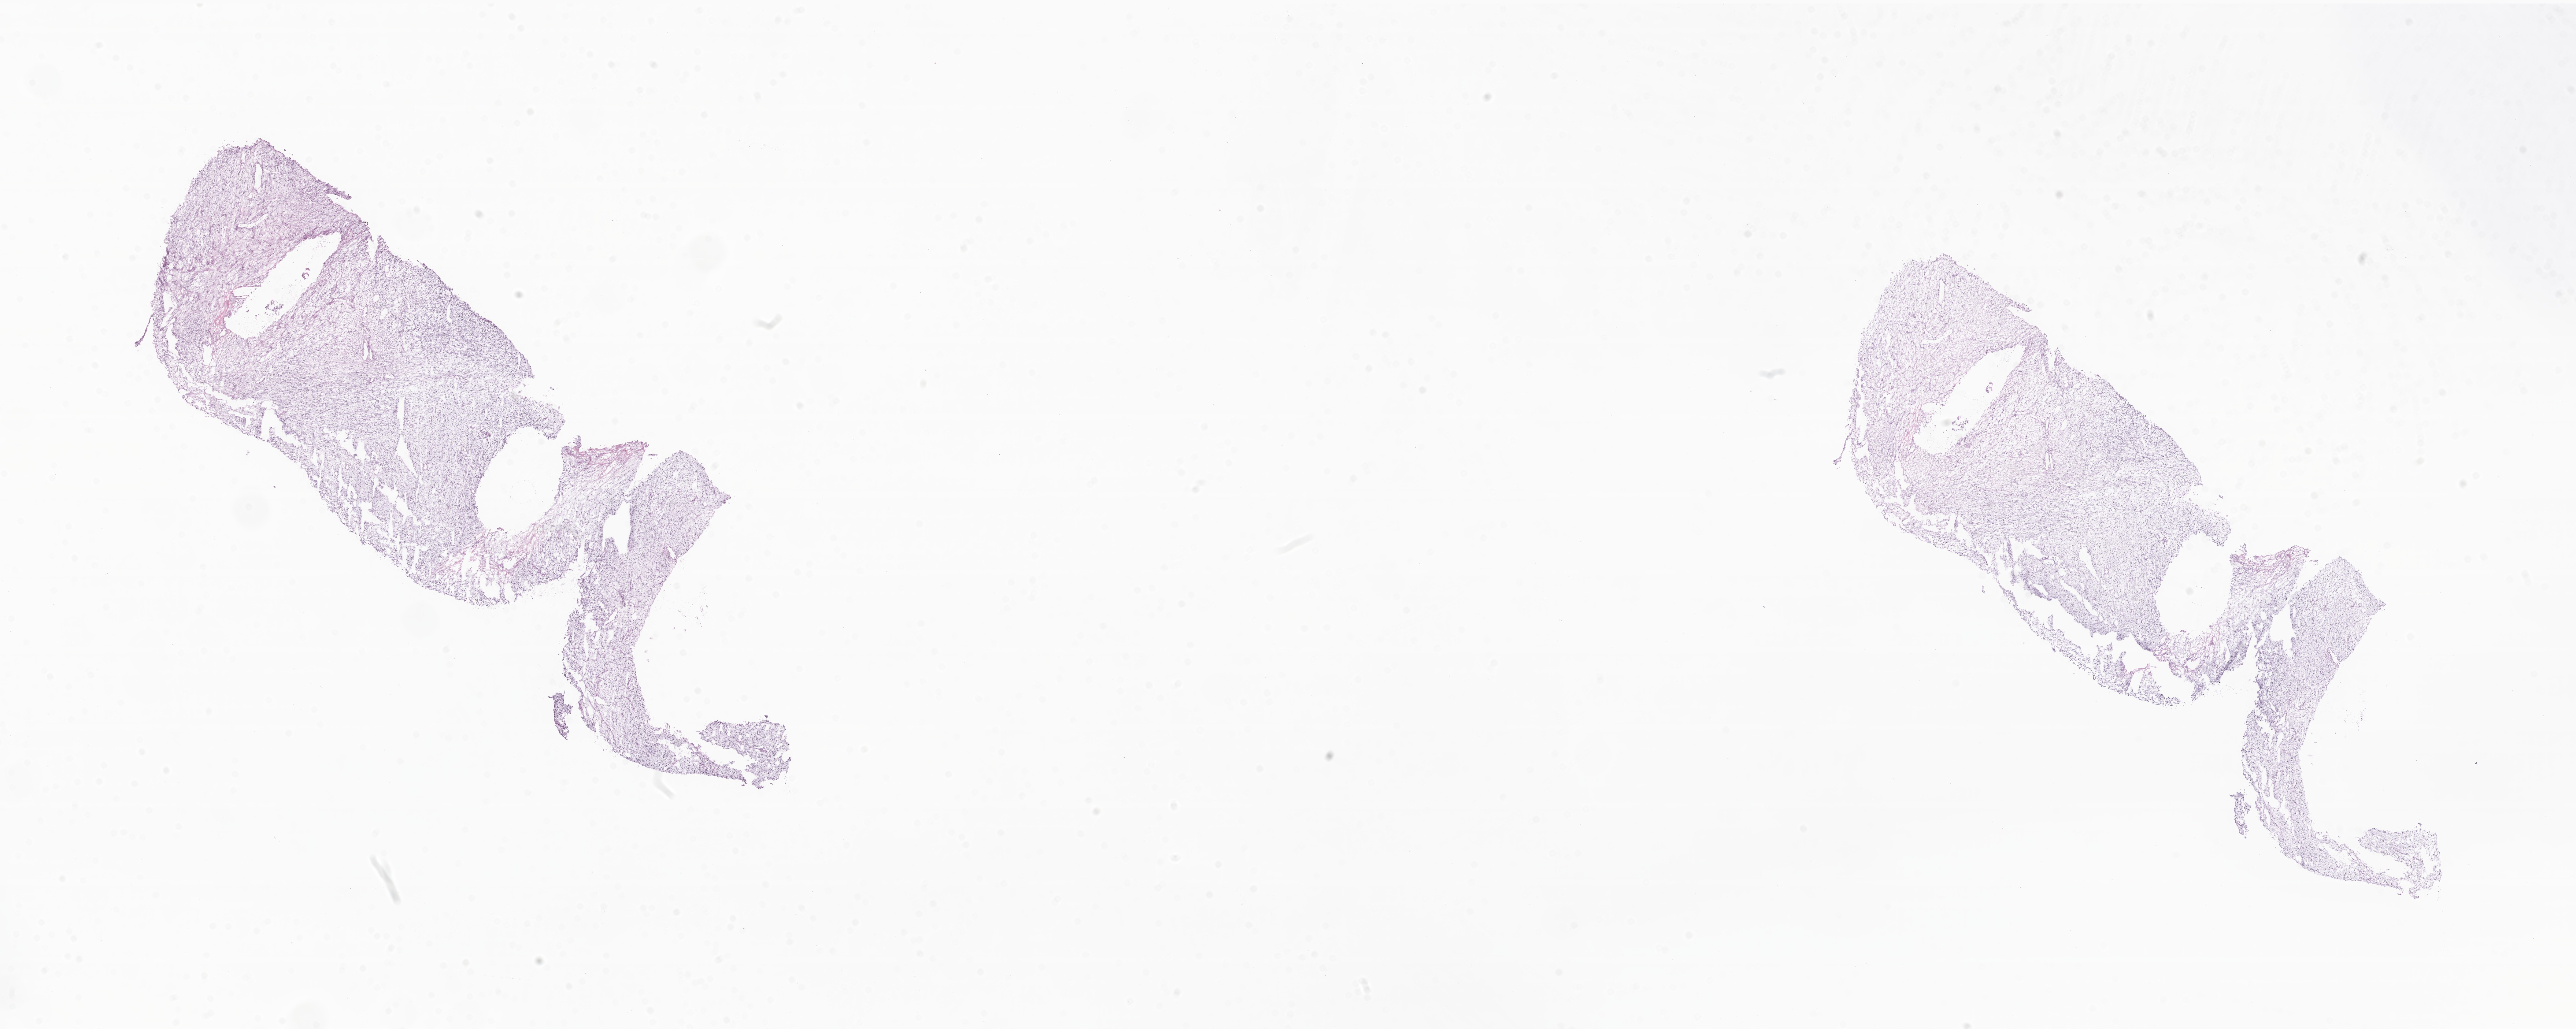
H&E whole-slide image of tumor tissue from the peritoneum — whole scanned area (about 35.5 x 14.2 mm) shown as a low-resolution overview; cryosection (OCT / tissue freezing medium). Patient: female, age 87 months (7 years 3 months).
Recorded diagnosis: Rhabdomyosarcoma, NOS.